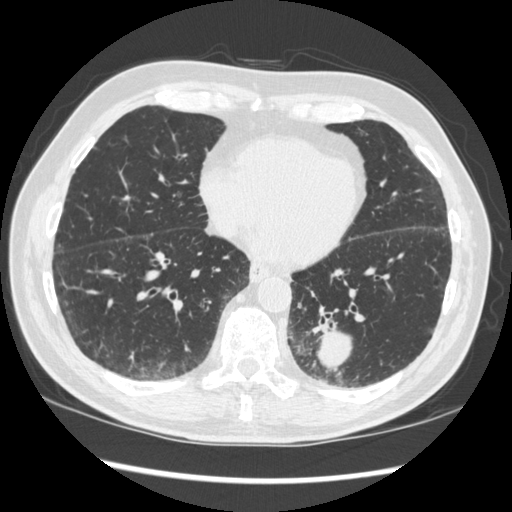
Low-dose screening chest CT, one axial slice; slice 117 of 348 in the series (ordered by position); reconstruction kernel STANDARD; lung window (W 1500 / L -600 HU); 1.25 mm slice thickness; 512 × 512 image matrix.
Outlined on this slice (outlined manually by an expert reader):
- lesion 1 (tumor, lower lobe of left lung): bounding box (x1, y1, x2, y2) in pixels: (317, 327, 352, 370)